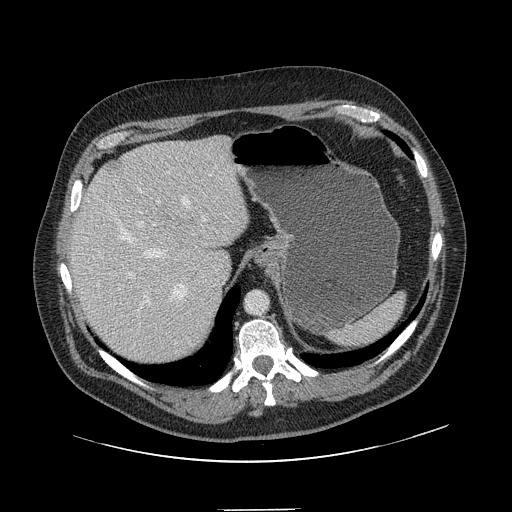
Contrast-enhanced abdominal CT, one axial slice; slice 112 of 154 in the series (ordered by position); 120 kVp; intravenous contrast given; soft-tissue window (W 400 / L 40 HU); 2.5 mm slice thickness; 512 × 512 image matrix, field of view 451 × 451 mm. Male patient, age 61 years. From the clinical record (not read from this slice): diagnosis: colorectal cancer liver metastases, imaged before liver resection; multiple liver metastases: yes; largest metastasis: 2.6 cm.
Annotated regions visible in this slice (expert manual segmentation):
- hepatic veins: bounding box <114,196,190,300> (left, top, right, bottom; pixels)
- liver: <71,137,247,365>
- planned liver remnant (the part of the liver to remain after resection): <72,145,247,357>
- portal vein (with intrahepatic branches): <120,200,206,310>